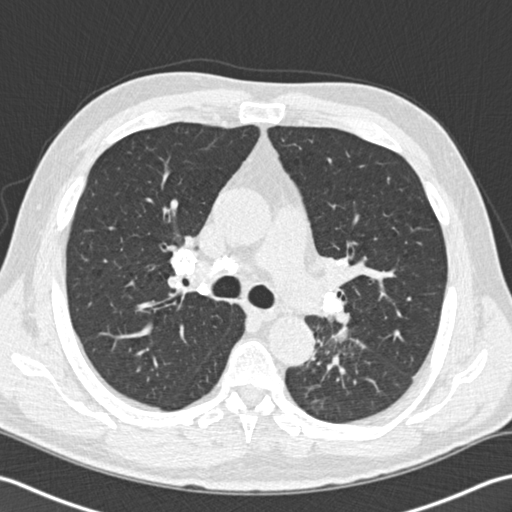
Low-dose screening chest CT, one axial slice; slice 111 of 170 in the series (ordered by position); reconstruction kernel B30f; 120 kVp; lung window (W 1500 / L -600 HU); 2 mm slice thickness; 512 × 512 image matrix.
Outlined on this slice (outlined manually by an expert reader):
- lesion 1 (tumor, lower lobe of left lung): bounding box [x1, y1, x2, y2] px = [332, 327, 348, 342]